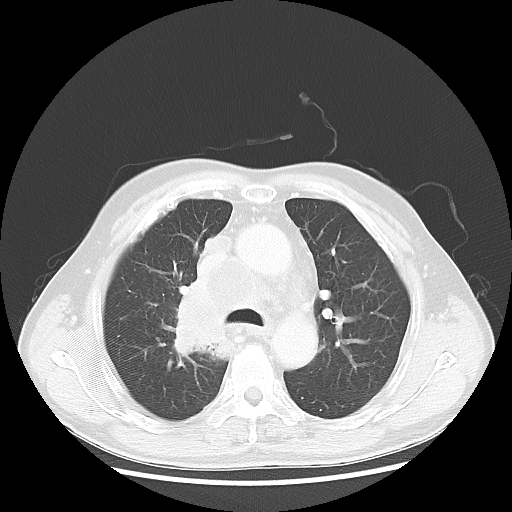
Chest CT, one axial slice; reconstruction kernel LUNG; 100 kVp; lung window (W 1500 / L -600 HU); 5 mm slice thickness; 512 × 512 image matrix. Patient: male, 64 years. Case-level facts recorded for this patient, not image findings: clinical TNM (as recorded): T3 N3 M0; histopathological grade: G3.
Annotated regions visible in this slice (bounding box drawn by a radiologist):
- lung tumour (recorded histology: small cell carcinoma): bounding box <169,277,229,372> (left, top, right, bottom; pixels)